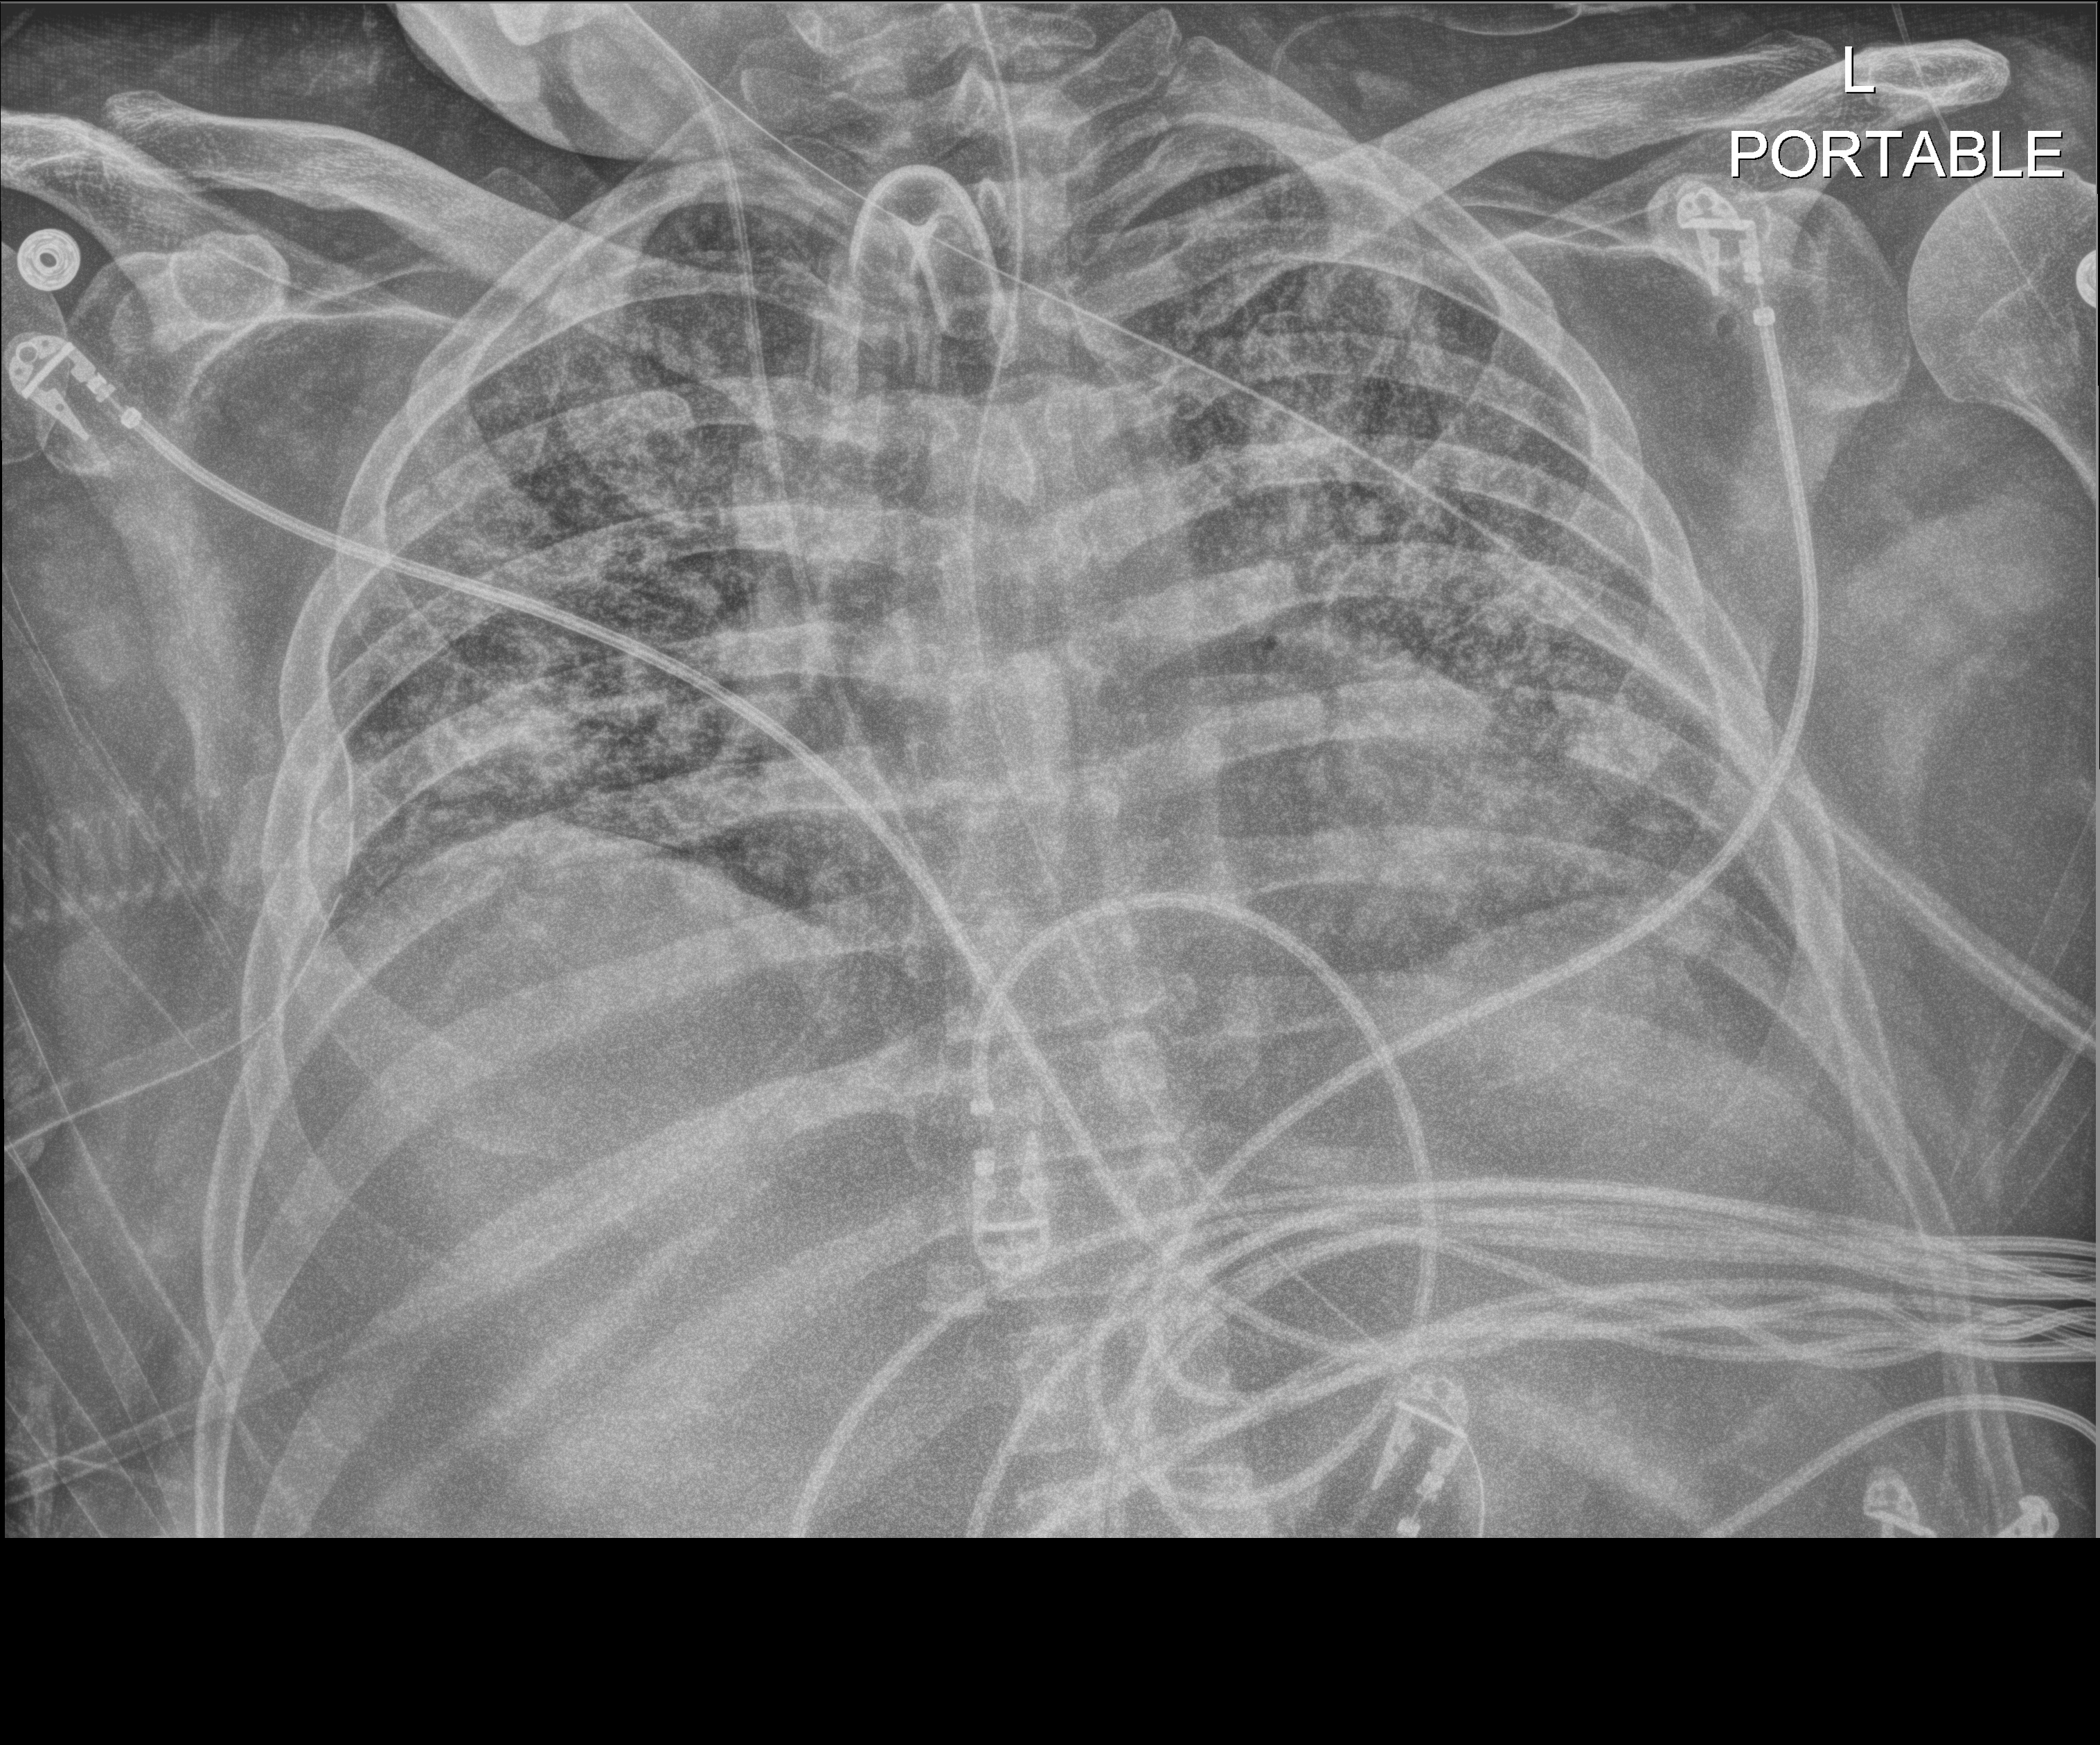
Chest radiograph (digital radiography); anteroposterior (AP) projection. Patient hospitalised with COVID-19; male, aged 18–59 years.
Hospital-stay facts (about this admission, not read from this image; timing relative to this image not recorded): mechanically ventilated during this hospital stay: yes; admitted to intensive care during this hospital stay: yes; hypertension (admission record): yes.